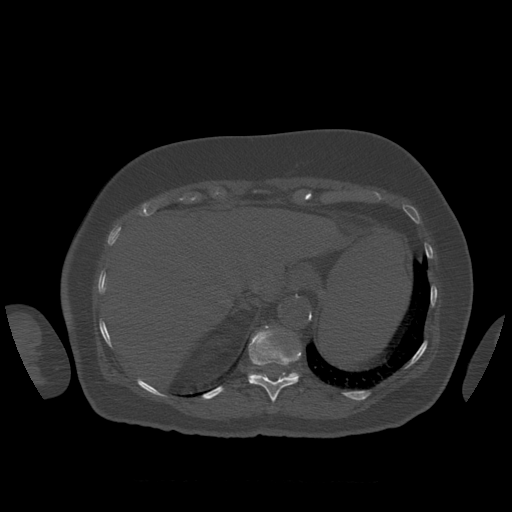
CT including the spine, one axial slice. Slice 318 of 399 in the series (ordered by position). Reconstruction kernel STANDARD. Bone window (W 1800 / L 400 HU). 1.25 mm slice thickness. 512 × 512 image matrix, field of view 404 × 404 mm. Patient age 81 years. Case-level facts recorded for this patient, not image findings: primary cancer: renal; vertebrae with lytic lesions (as recorded): L1.
Annotated regions visible in this slice (semi-automatic segmentation, software-assisted and operator-edited):
- T11 vertebra: box from (x=249, y=326) to (x=302, y=402) px
- T12 vertebra: (x=248, y=372)–(x=300, y=378)